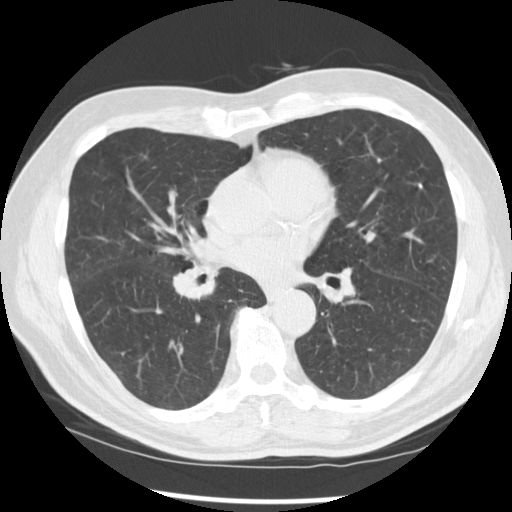
Axial slice from a low-dose chest CT screening exam. Baseline annual screen. Lung window (W 1500 / L -600 HU). 120 kVp. Slice 142 of 277 in the series. Male participant, aged 67 years at enrolment. Current smoker at enrolment.
Lesion marked by an expert reader, bounding box [x1, y1, x2, y2] px = [156, 246, 228, 313]. Screening reader's record for this exam (one nodule recorded; not confirmed to be the boxed lesion): non-calcified nodule or mass ≥4 mm, left lower lobe, 15 × 15 mm, spiculated (stellate) margins, soft tissue attenuation. Note: the box lies in the patient's right hemithorax on this image, whereas the reader's record names the left lung; they may be different findings. Official screen result: positive, change unspecified: nodule(s) >= 4 mm or enlarging nodule(s), mass(es), or other non-specific abnormalities suspicious for lung cancer. Participant outcome: lung cancer diagnosed 49 days after this screen — squamous cell carcinoma, NOS, right middle lobe, poorly differentiated (G3), stage IIB (AJCC 6th edition), 35 mm at pathology.